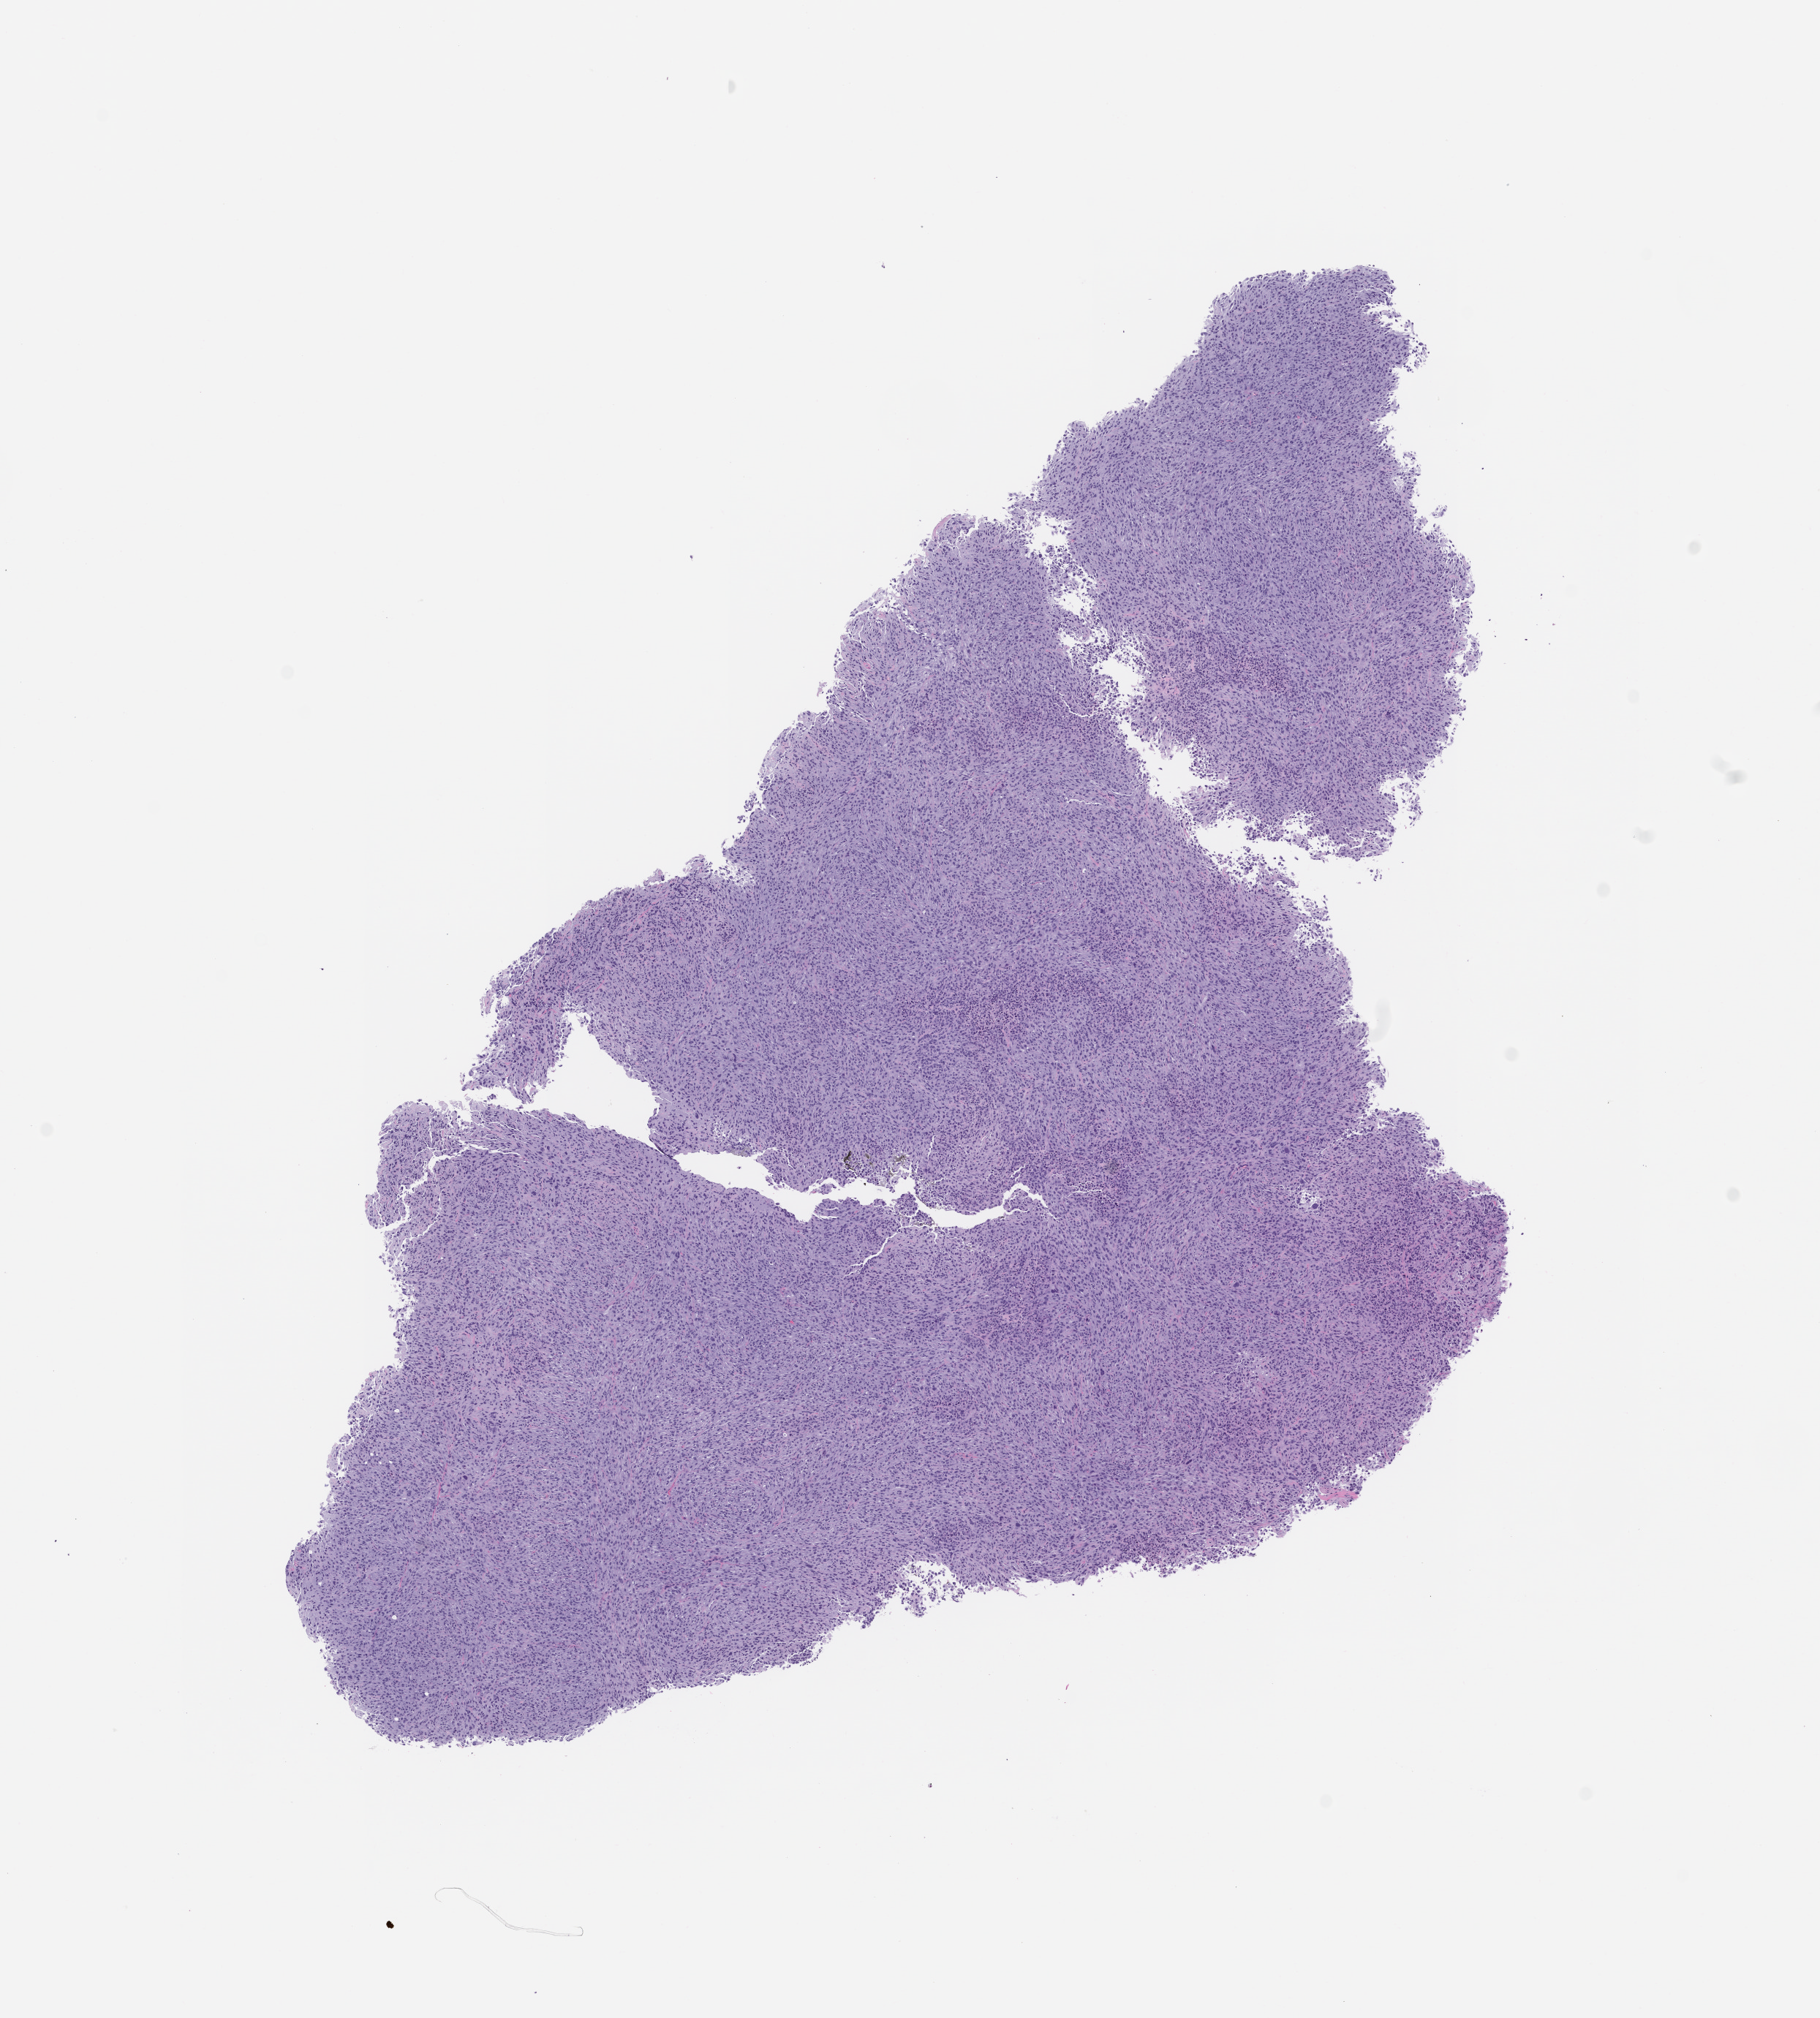
H&E whole-slide image of a patient-derived xenograft (PDX) tumor grown in a mouse, passage 1 — shown as a low-resolution overview of the whole scanned area (about 10.0 x 11.1 mm), formalin-fixed paraffin-embedded section, tumor site category: thyroid.
- originating patient diagnosis: Thyroid Gland Oncocytic Carcinoma